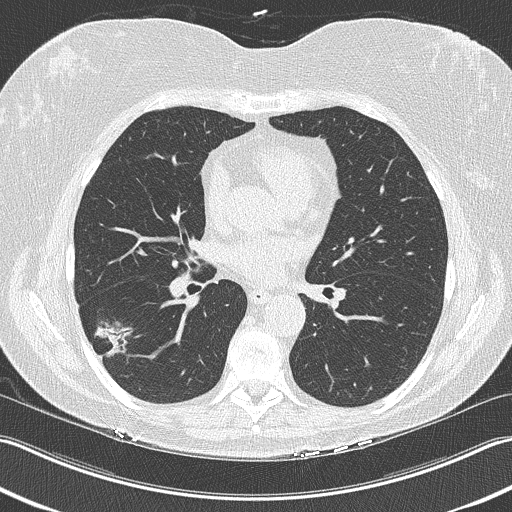
Low-dose screening chest CT, one axial slice. Position 117 of 210 along the scan axis. 120 kVp. Lung window (W 1500 / L -600 HU). 512 × 512 image matrix, field of view 348 × 348 mm.
Structures marked on this image (manually delineated by an expert):
- lesion 1 (tumor, lower lobe of right lung): bounding box <94,321,135,357> (left, top, right, bottom; pixels)